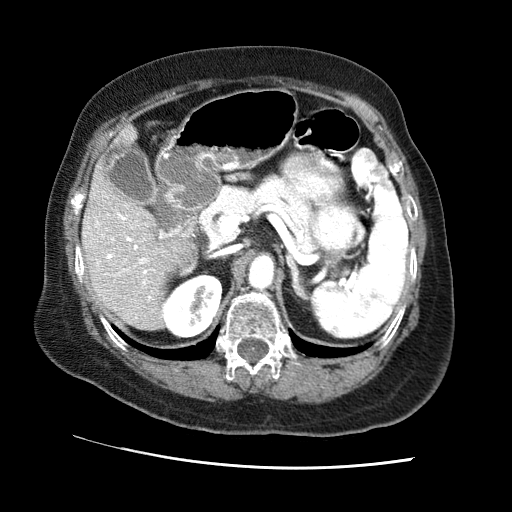
Contrast-enhanced abdominal CT (liver protocol), one axial slice. Slice 31 of 65 in the series (ordered by position). Reconstruction kernel STANDARD. 120 kVp. Soft-tissue window (W 400 / L 40 HU). 2.5 mm slice thickness. 512 × 512 image matrix. Case-level facts recorded for this patient, not image findings: diagnosis: hepatocellular carcinoma (patient treated with transarterial chemoembolisation; whether this scan precedes or follows treatment is not stated here); TNM stage (as recorded): Stage-II; Child-Pugh class: A.
Annotated regions visible in this slice (semi-automatic segmentation, software-assisted and operator-edited):
- liver parenchyma outside the tumour (the mass and vessels are separate outlines, so this box may not span the whole liver): bounding box <82,126,196,330> (left, top, right, bottom; pixels)
- liver vessels: <84,205,163,317>